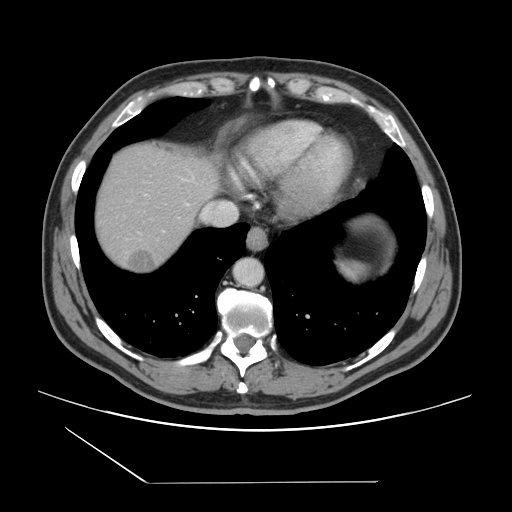
Contrast-enhanced abdominal CT, one axial slice; intravenous contrast given; soft-tissue window (W 400 / L 40 HU); 2.5 mm slice thickness; 512 × 512 image matrix, field of view 407 × 407 mm. Male patient, age 61 years. Case-level facts recorded for this patient, not image findings: diagnosis: colorectal cancer liver metastases, imaged before liver resection; multiple liver metastases: yes; largest metastasis: 5.5 cm.
Annotated regions visible in this slice (outlined manually by an expert reader):
- liver: box from (x=94, y=145) to (x=215, y=273) px
- planned liver remnant (the part of the liver to remain after resection): (x=94, y=145)–(x=214, y=232)
- liver metastasis: (x=126, y=249)–(x=158, y=271)